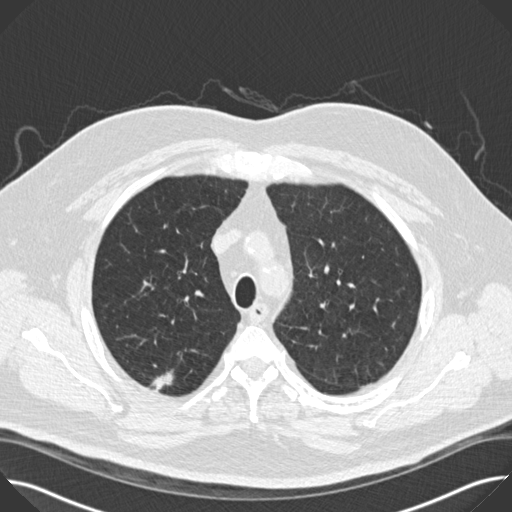
Chest CT (low-dose screening protocol), one axial image; first (baseline) screen; lung window (W 1500 / L -600 HU); 2 mm slice thickness; slice 123 of 158 in the series. Male, age 65 years at enrolment. Former smoker at enrolment.
Expert-annotated lung lesion, bounding box <148,360,190,417> (left, top, right, bottom; pixels). The screening reader recorded 2 non-calcified nodules or masses ≥4 mm on this exam (right upper lobe, right upper lobe); which of them this box marks is not recorded. Official screen result: positive, change unspecified: nodule(s) >= 4 mm or enlarging nodule(s), mass(es), or other non-specific abnormalities suspicious for lung cancer. Participant outcome: lung cancer diagnosed 47 days after this screen — bronchiolo-alveolar adenocarcinoma, NOS, right upper lobe, moderately differentiated (G2), stage IIA (AJCC 6th edition), 14 mm at pathology.